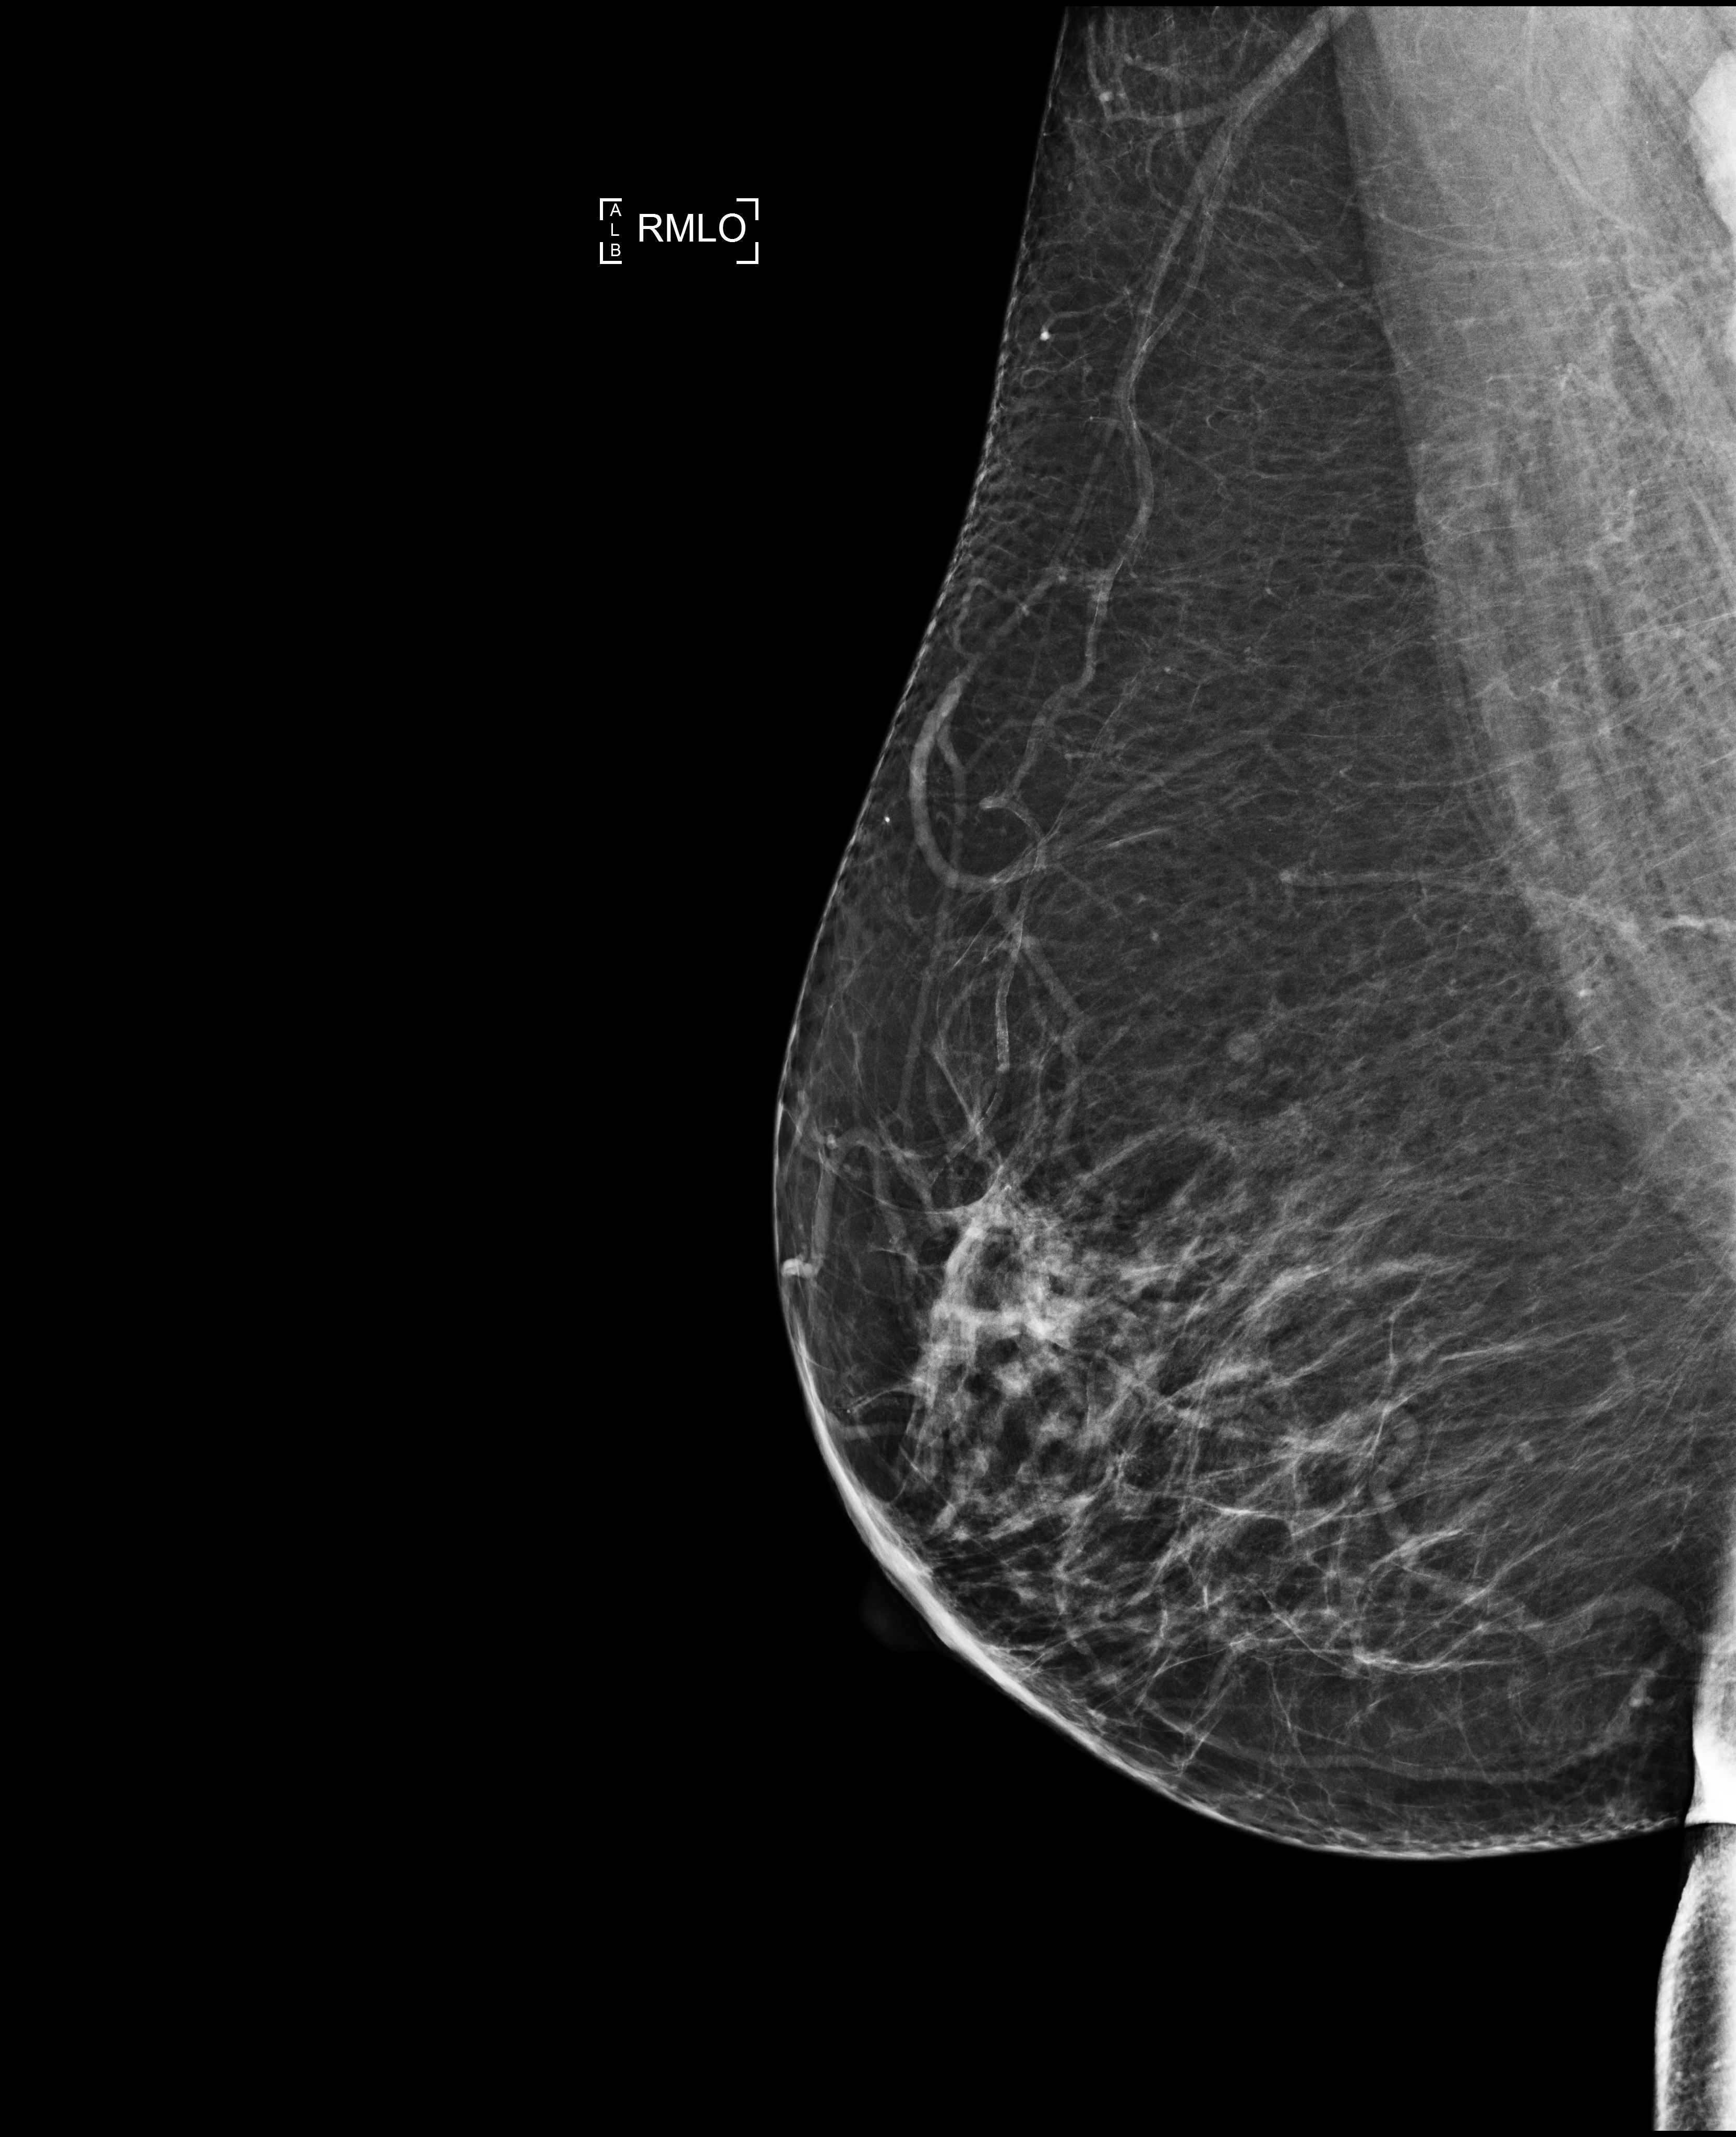
Screening examination, compressed breast thickness 70 mm, system: Selenia Dimensions. Female patient, age 62 years.
Image type: full-field digital mammogram. Breast: right. Projection: mediolateral oblique (MLO) view.